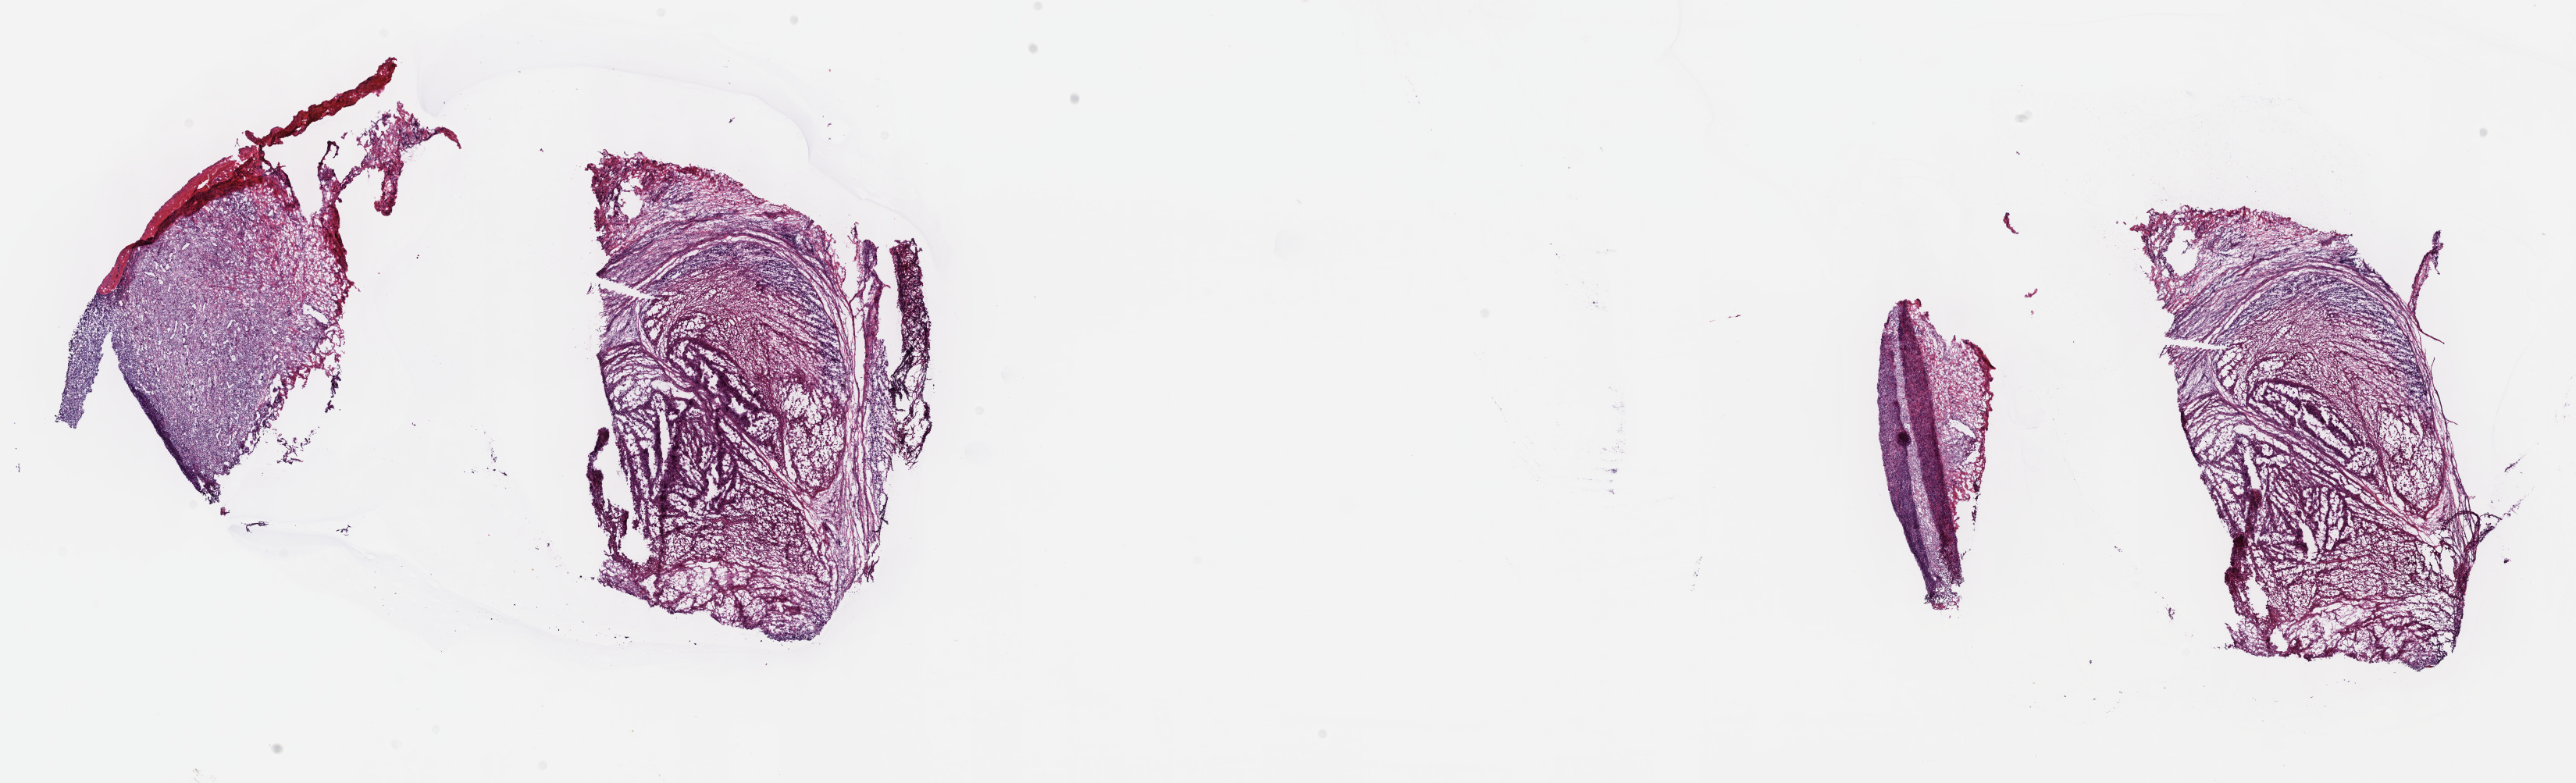
H&E-stained whole-slide image, shown as a low-resolution overview of the whole scanned area (about 26.7 x 8.1 mm); frozen section; sample: primary tumour, connective, subcutaneous and other soft tissues. Female, age 49 years at initial diagnosis. Slide review estimates, as recorded: tumour cells 90%, tumour nuclei 90%, normal cells 0%, stromal cells 10%, necrosis 0%. Inflammatory infiltration, as recorded: lymphocyte infiltration 0%, monocyte infiltration 0%, neutrophil infiltration 0%.
Diagnosis: Undifferentiated sarcoma (connective, subcutaneous and other soft tissues of lower limb and hip).